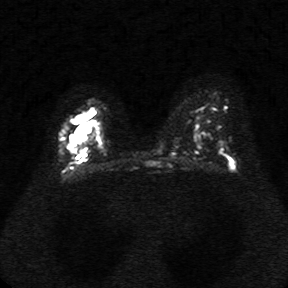
Breast MRI, one axial slice; slice 22 of 34 in the series (ordered by position); diffusion-weighted series; image 2 of 4 stored at this slice position (different b-values; order by instance number); 1.5 T; 5 mm slice thickness; 288 × 288 image matrix, field of view 340 × 340 mm. Female patient.
Annotated regions visible in this slice (outlined manually by an expert reader):
- tumour on diffusion-weighted imaging: bounding box [x1, y1, x2, y2] px = [67, 105, 98, 154]